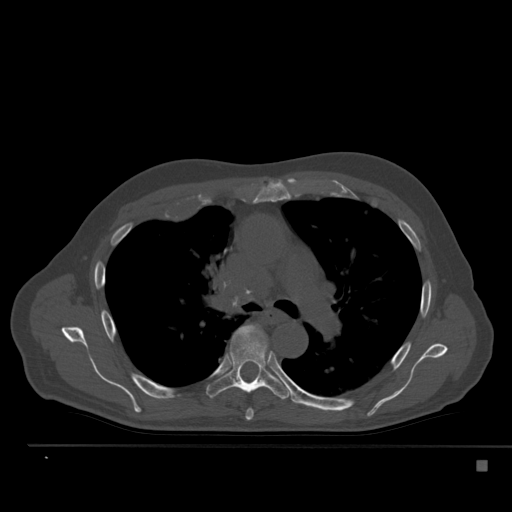
CT including the spine, one axial slice. Reconstruction kernel Br40s. 120 kVp. Bone window (W 1800 / L 400 HU). 512 × 512 image matrix, field of view 408 × 408 mm. Male patient, age 70 years. Case-level facts recorded for this patient, not image findings: primary cancer: renal; vertebrae with lytic lesions (as recorded): T4, T6, T10, T12, L3, L4, L5.
Annotated regions visible in this slice (semi-automatic segmentation, software-assisted and operator-edited):
- T5 vertebra: bounding box <245,409,254,421> (left, top, right, bottom; pixels)
- T6 vertebra: <206,324,291,400>